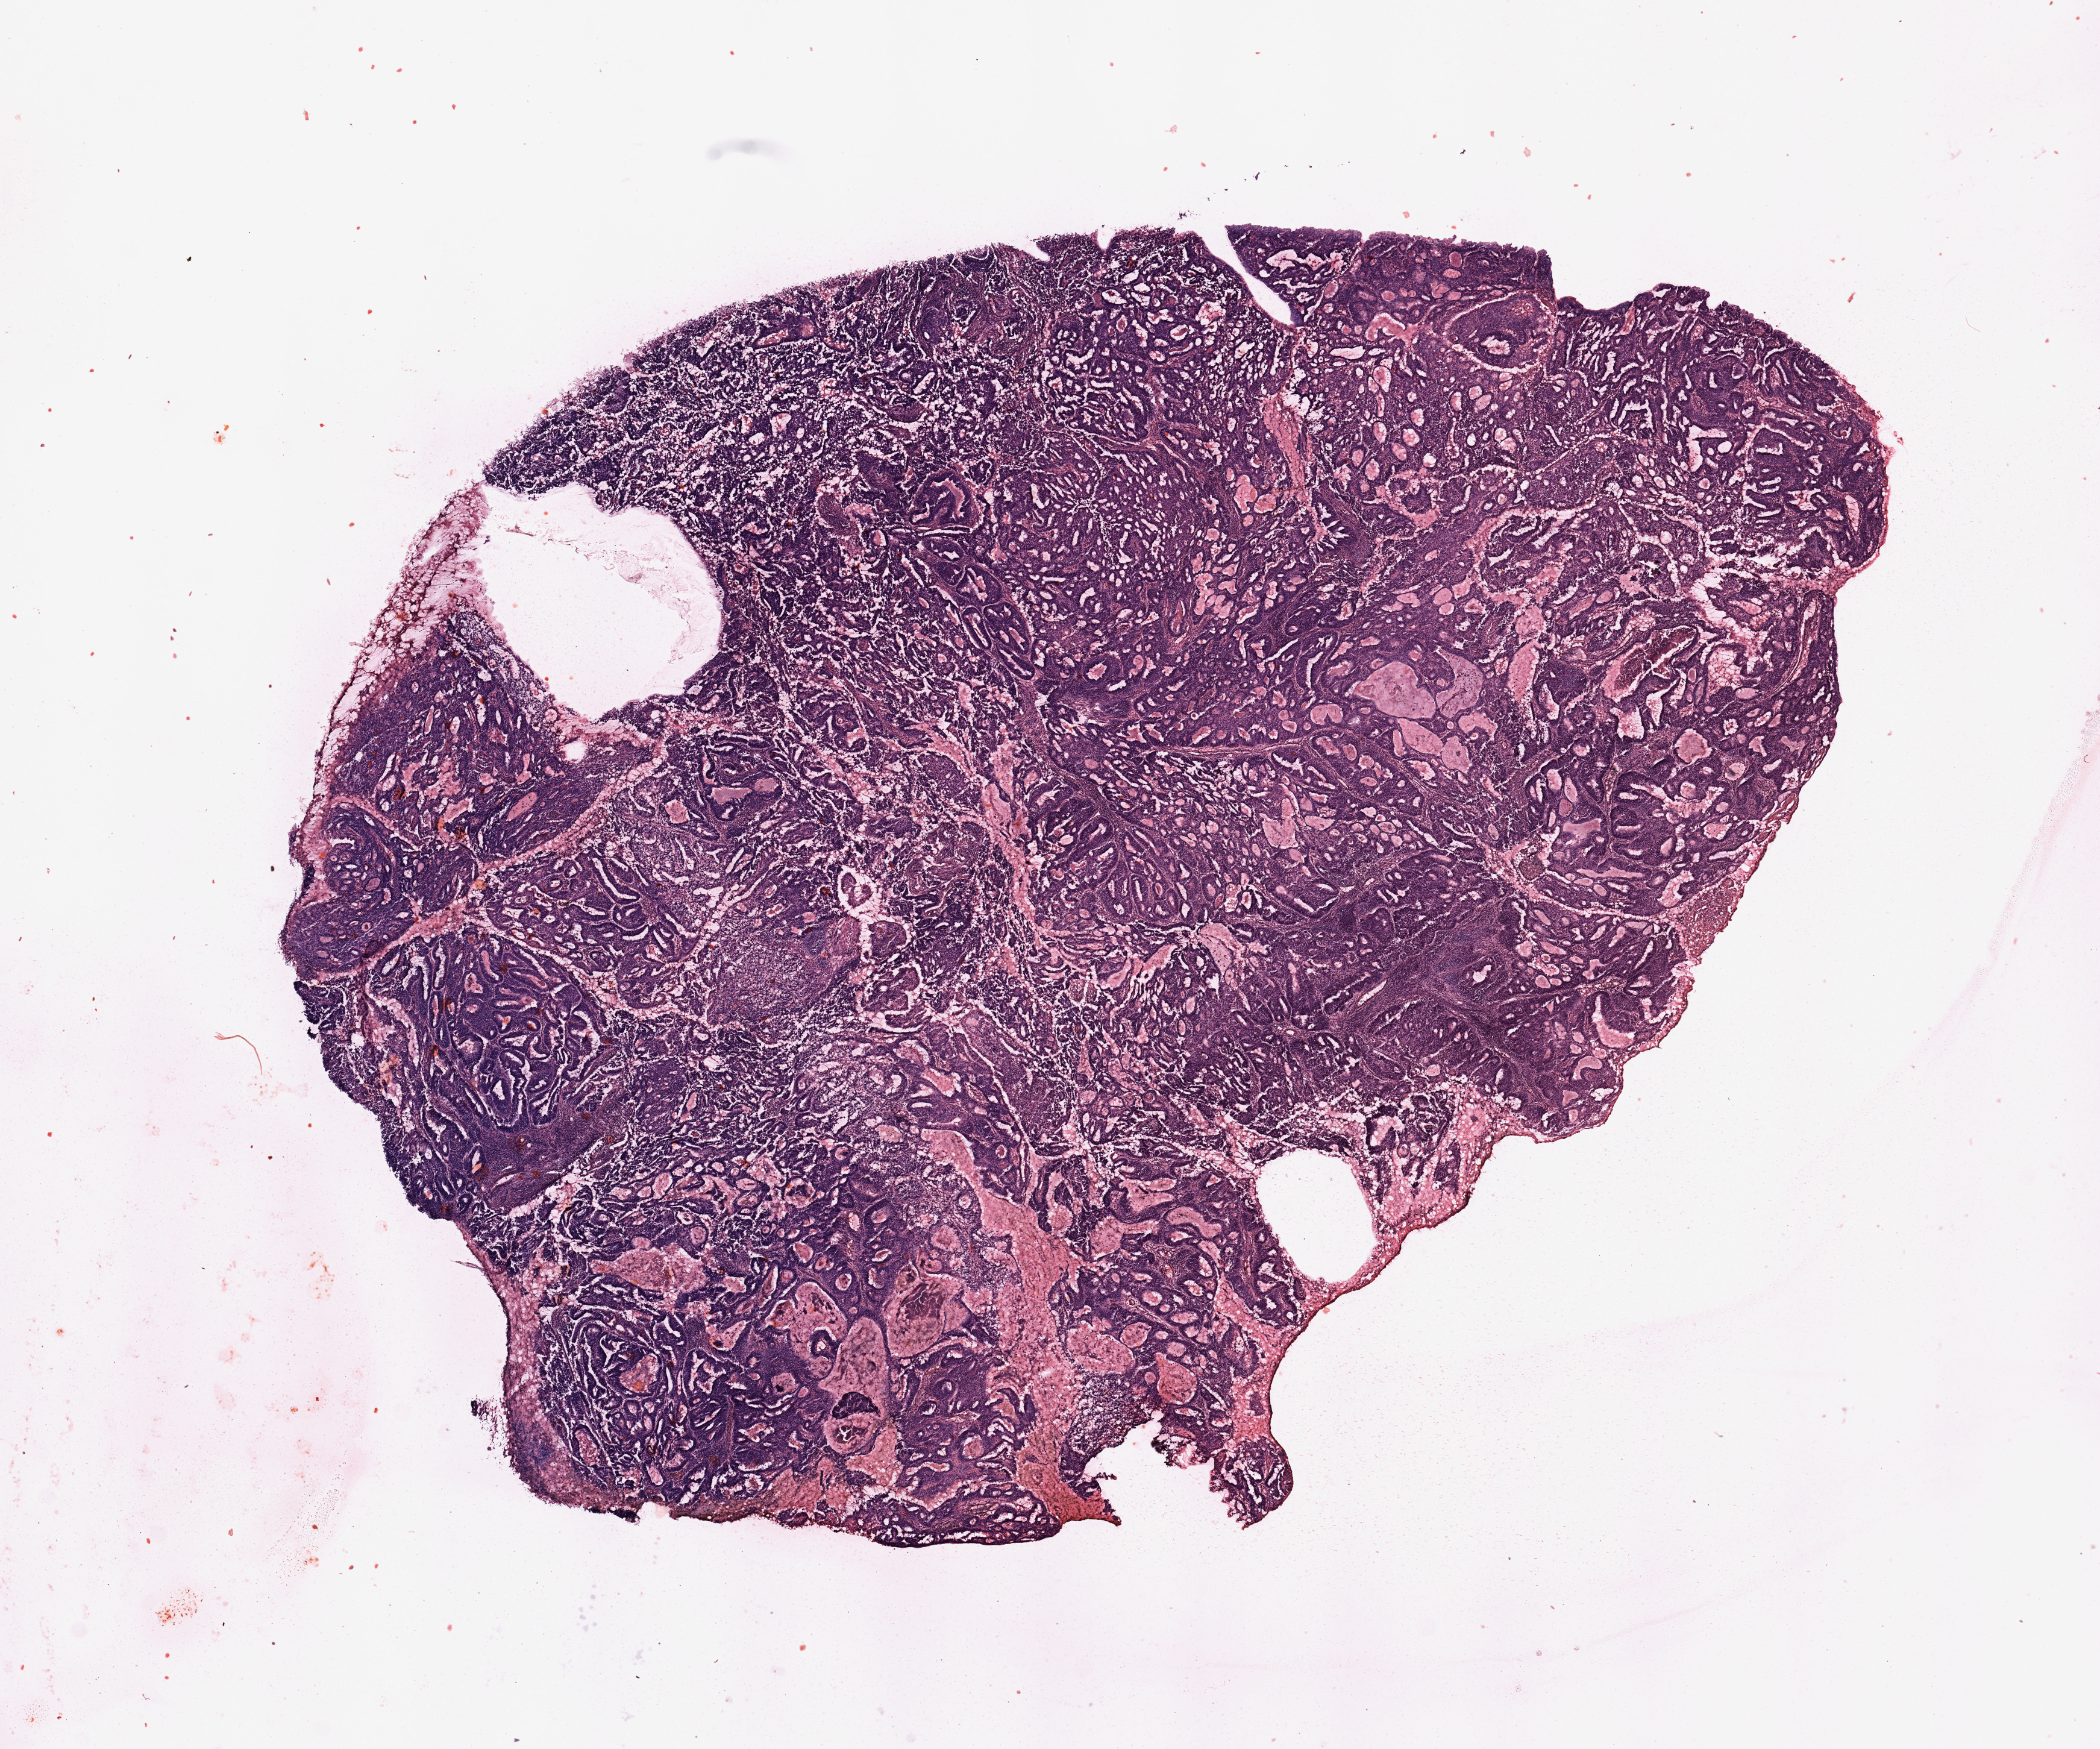
Whole-slide histology image, H&E-stained — low-resolution overview of the scanned area, about 13.8 x 11.5 mm (slide scanned at 20x). Tumour tissue sample, uterus. Female, 66 y/o. Histologic grade: G2 (moderately differentiated).
AJCC pathologic stage: I. Diagnosis: Endometrioid adenocarcinoma, NOS.